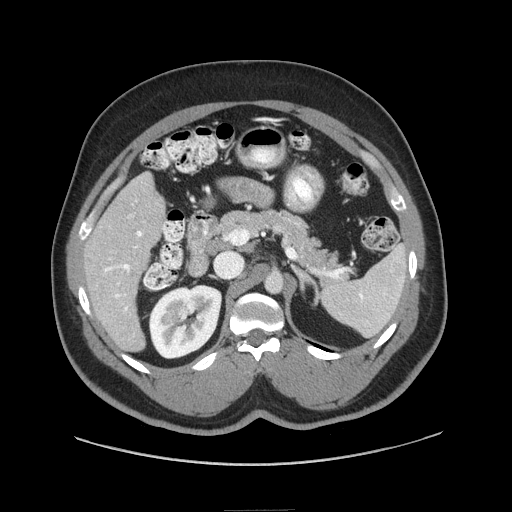
Contrast-enhanced abdominal CT (liver protocol), one axial slice. Slice 37 of 87 in the series (ordered by position). 140 kVp. Soft-tissue window (W 400 / L 40 HU). 2.5 mm slice thickness. 512 × 512 image matrix, field of view 440 × 440 mm. Case-level facts recorded for this patient, not image findings: diagnosis: hepatocellular carcinoma (patient treated with transarterial chemoembolisation; whether this scan precedes or follows treatment is not stated here); TNM stage (as recorded): Stage-II; Child-Pugh class: A; tumour nodularity: uninodular.
Structures marked on this image (semi-automatically segmented with operator editing):
- liver parenchyma outside the tumour (the mass and vessels are separate outlines, so this box may not span the whole liver): bounding box (x1, y1, x2, y2) in pixels: (84, 172, 166, 350)
- liver vessels: (103, 215, 142, 312)